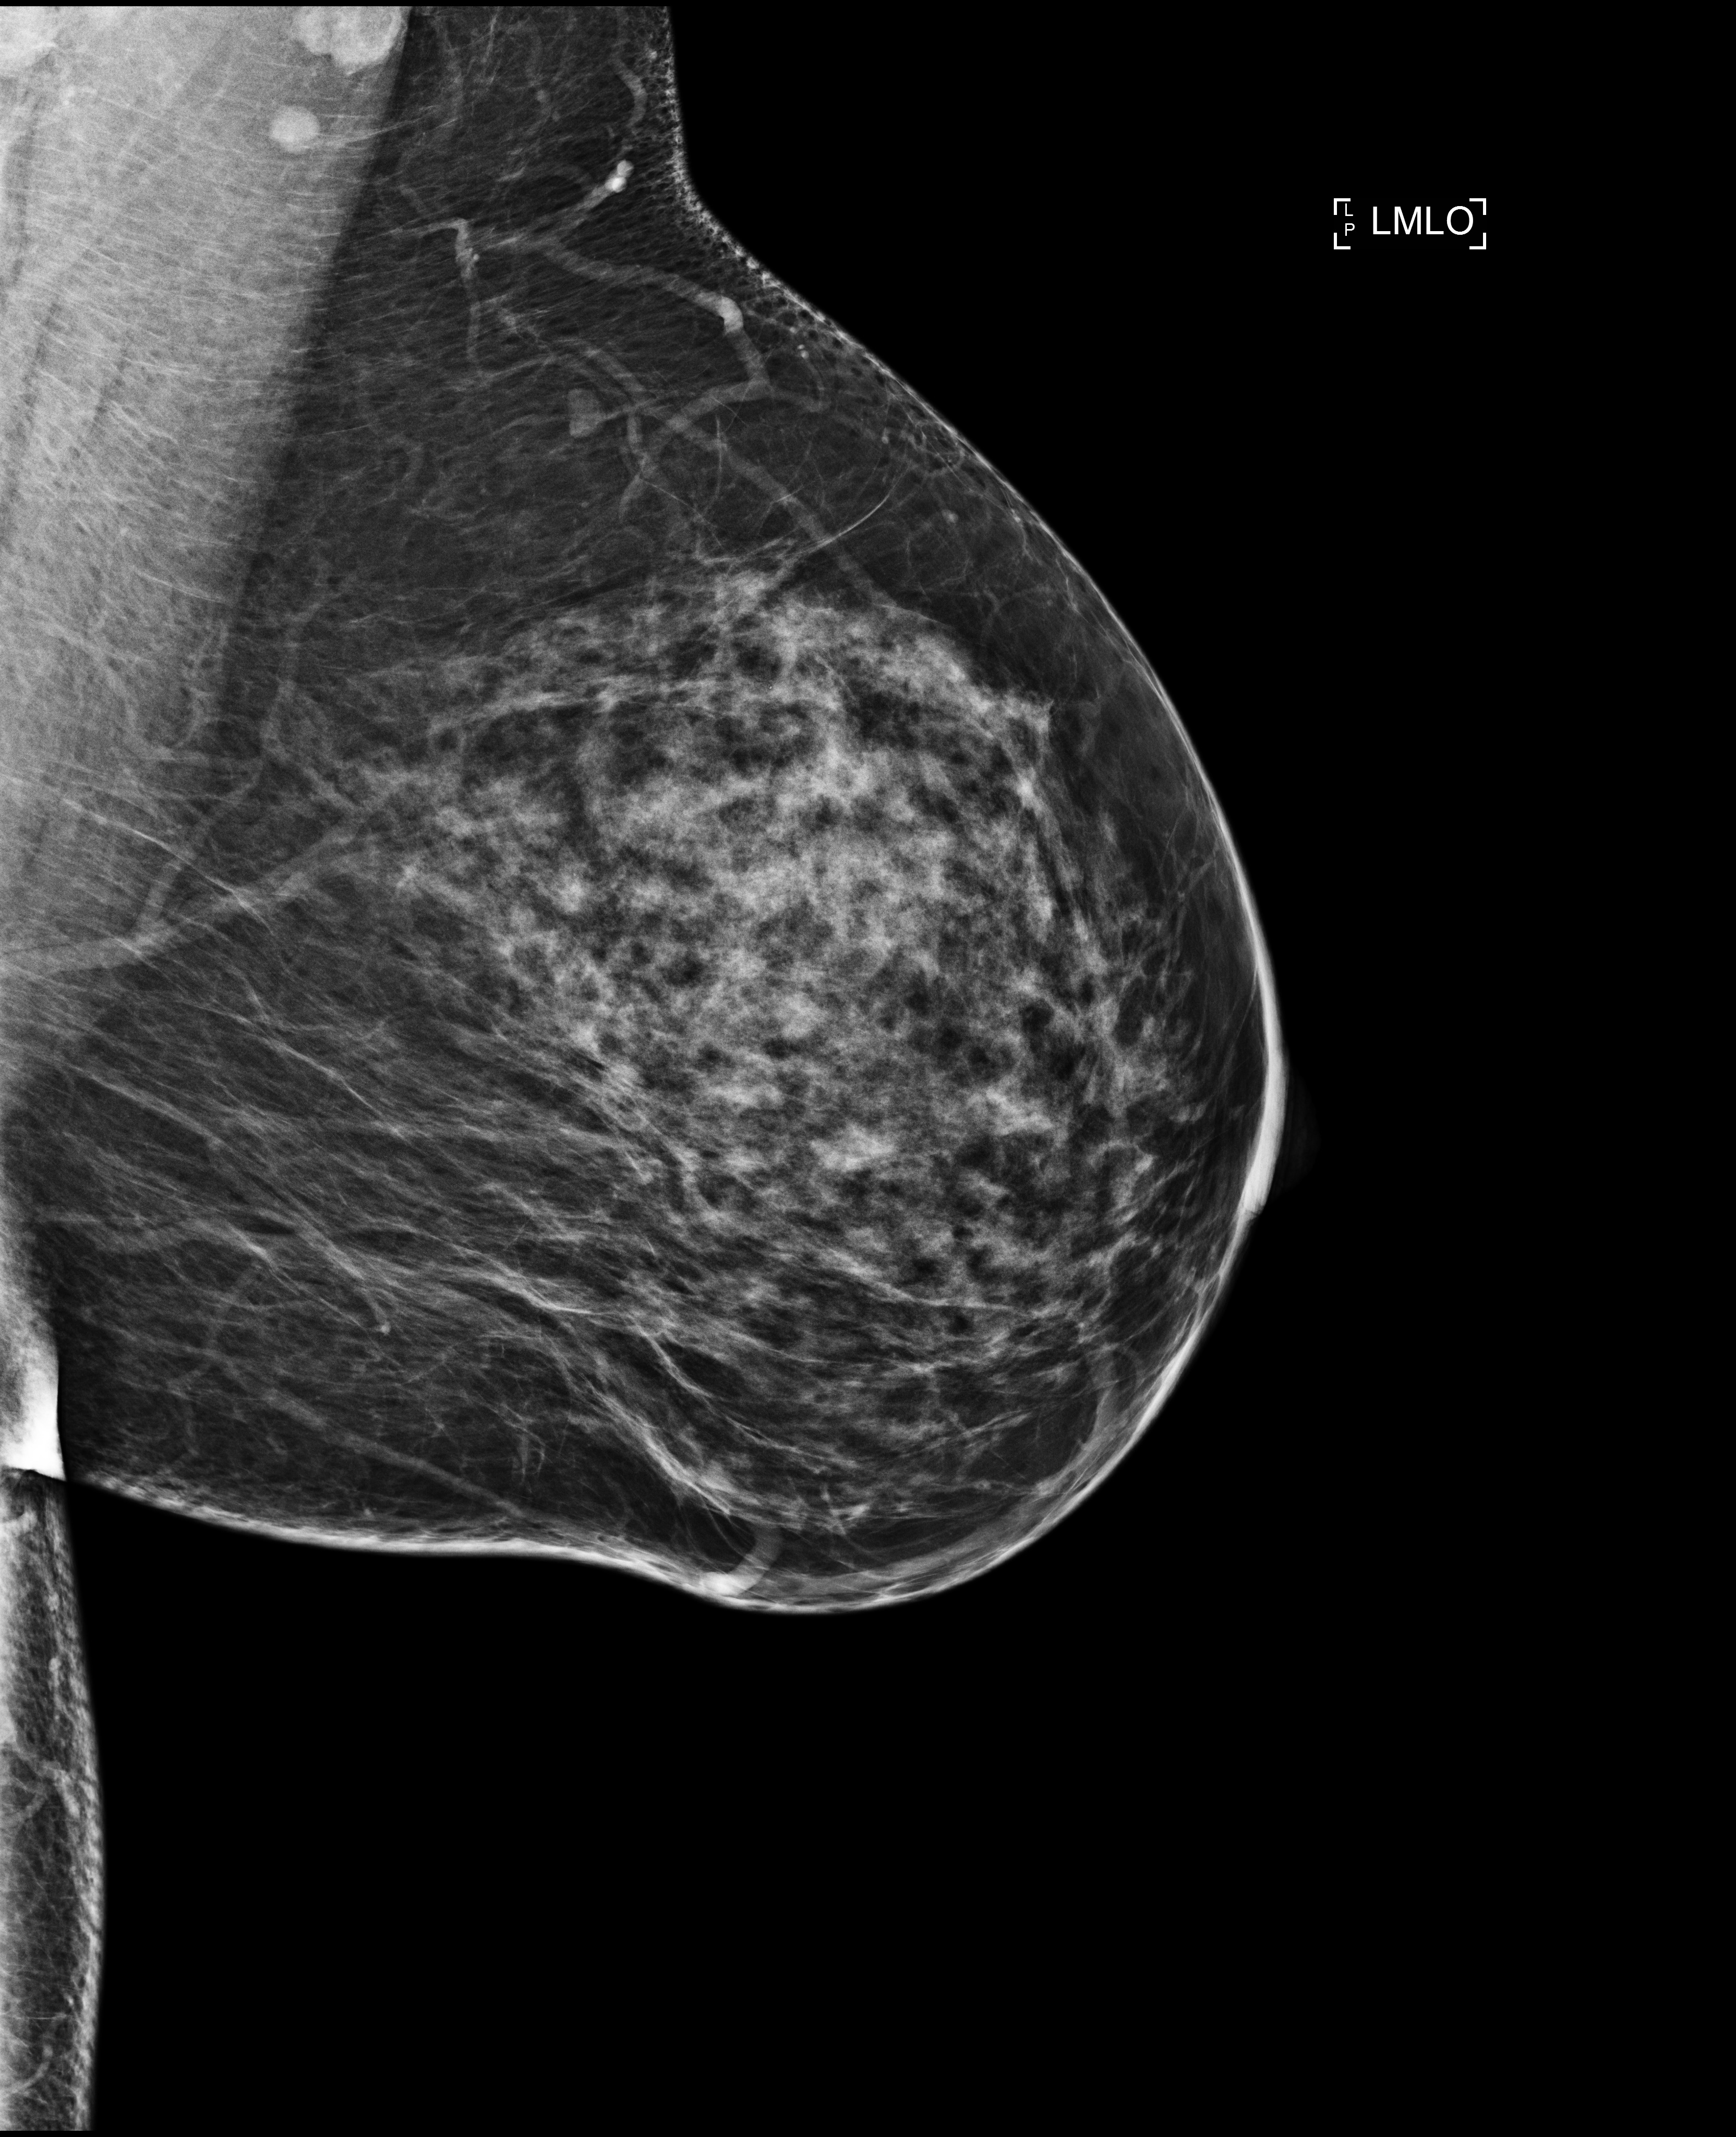
Screening examination; system: Selenia Dimensions. Female patient, age 50 years.
Image type: full-field digital mammogram. Breast: left. Projection: MLO view.